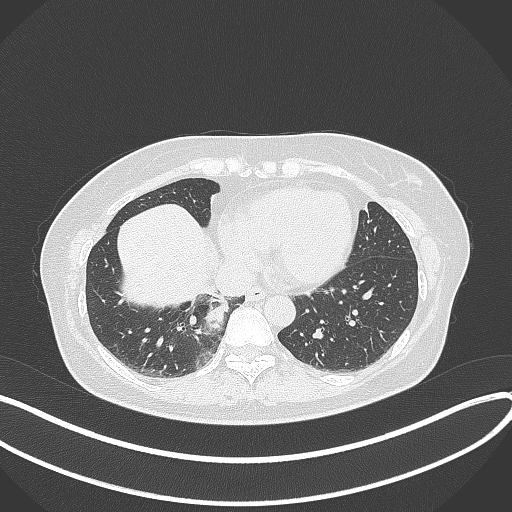
Chest CT, one axial slice. Position 105 of 331 along the scan axis. Reconstruction kernel B70f. Lung window (W 1500 / L -600 HU). 1 mm slice thickness. 512 × 512 image matrix, field of view 400 × 400 mm. Patient: female, 54 years. From the clinical record (not read from this slice): clinical TNM (as recorded): T4 N0 M0.
Structures marked on this image (rectangle marked by the reading radiologist):
- lung tumour (recorded histology: adenocarcinoma): bounding box (x1, y1, x2, y2) in pixels: (201, 296, 230, 336)